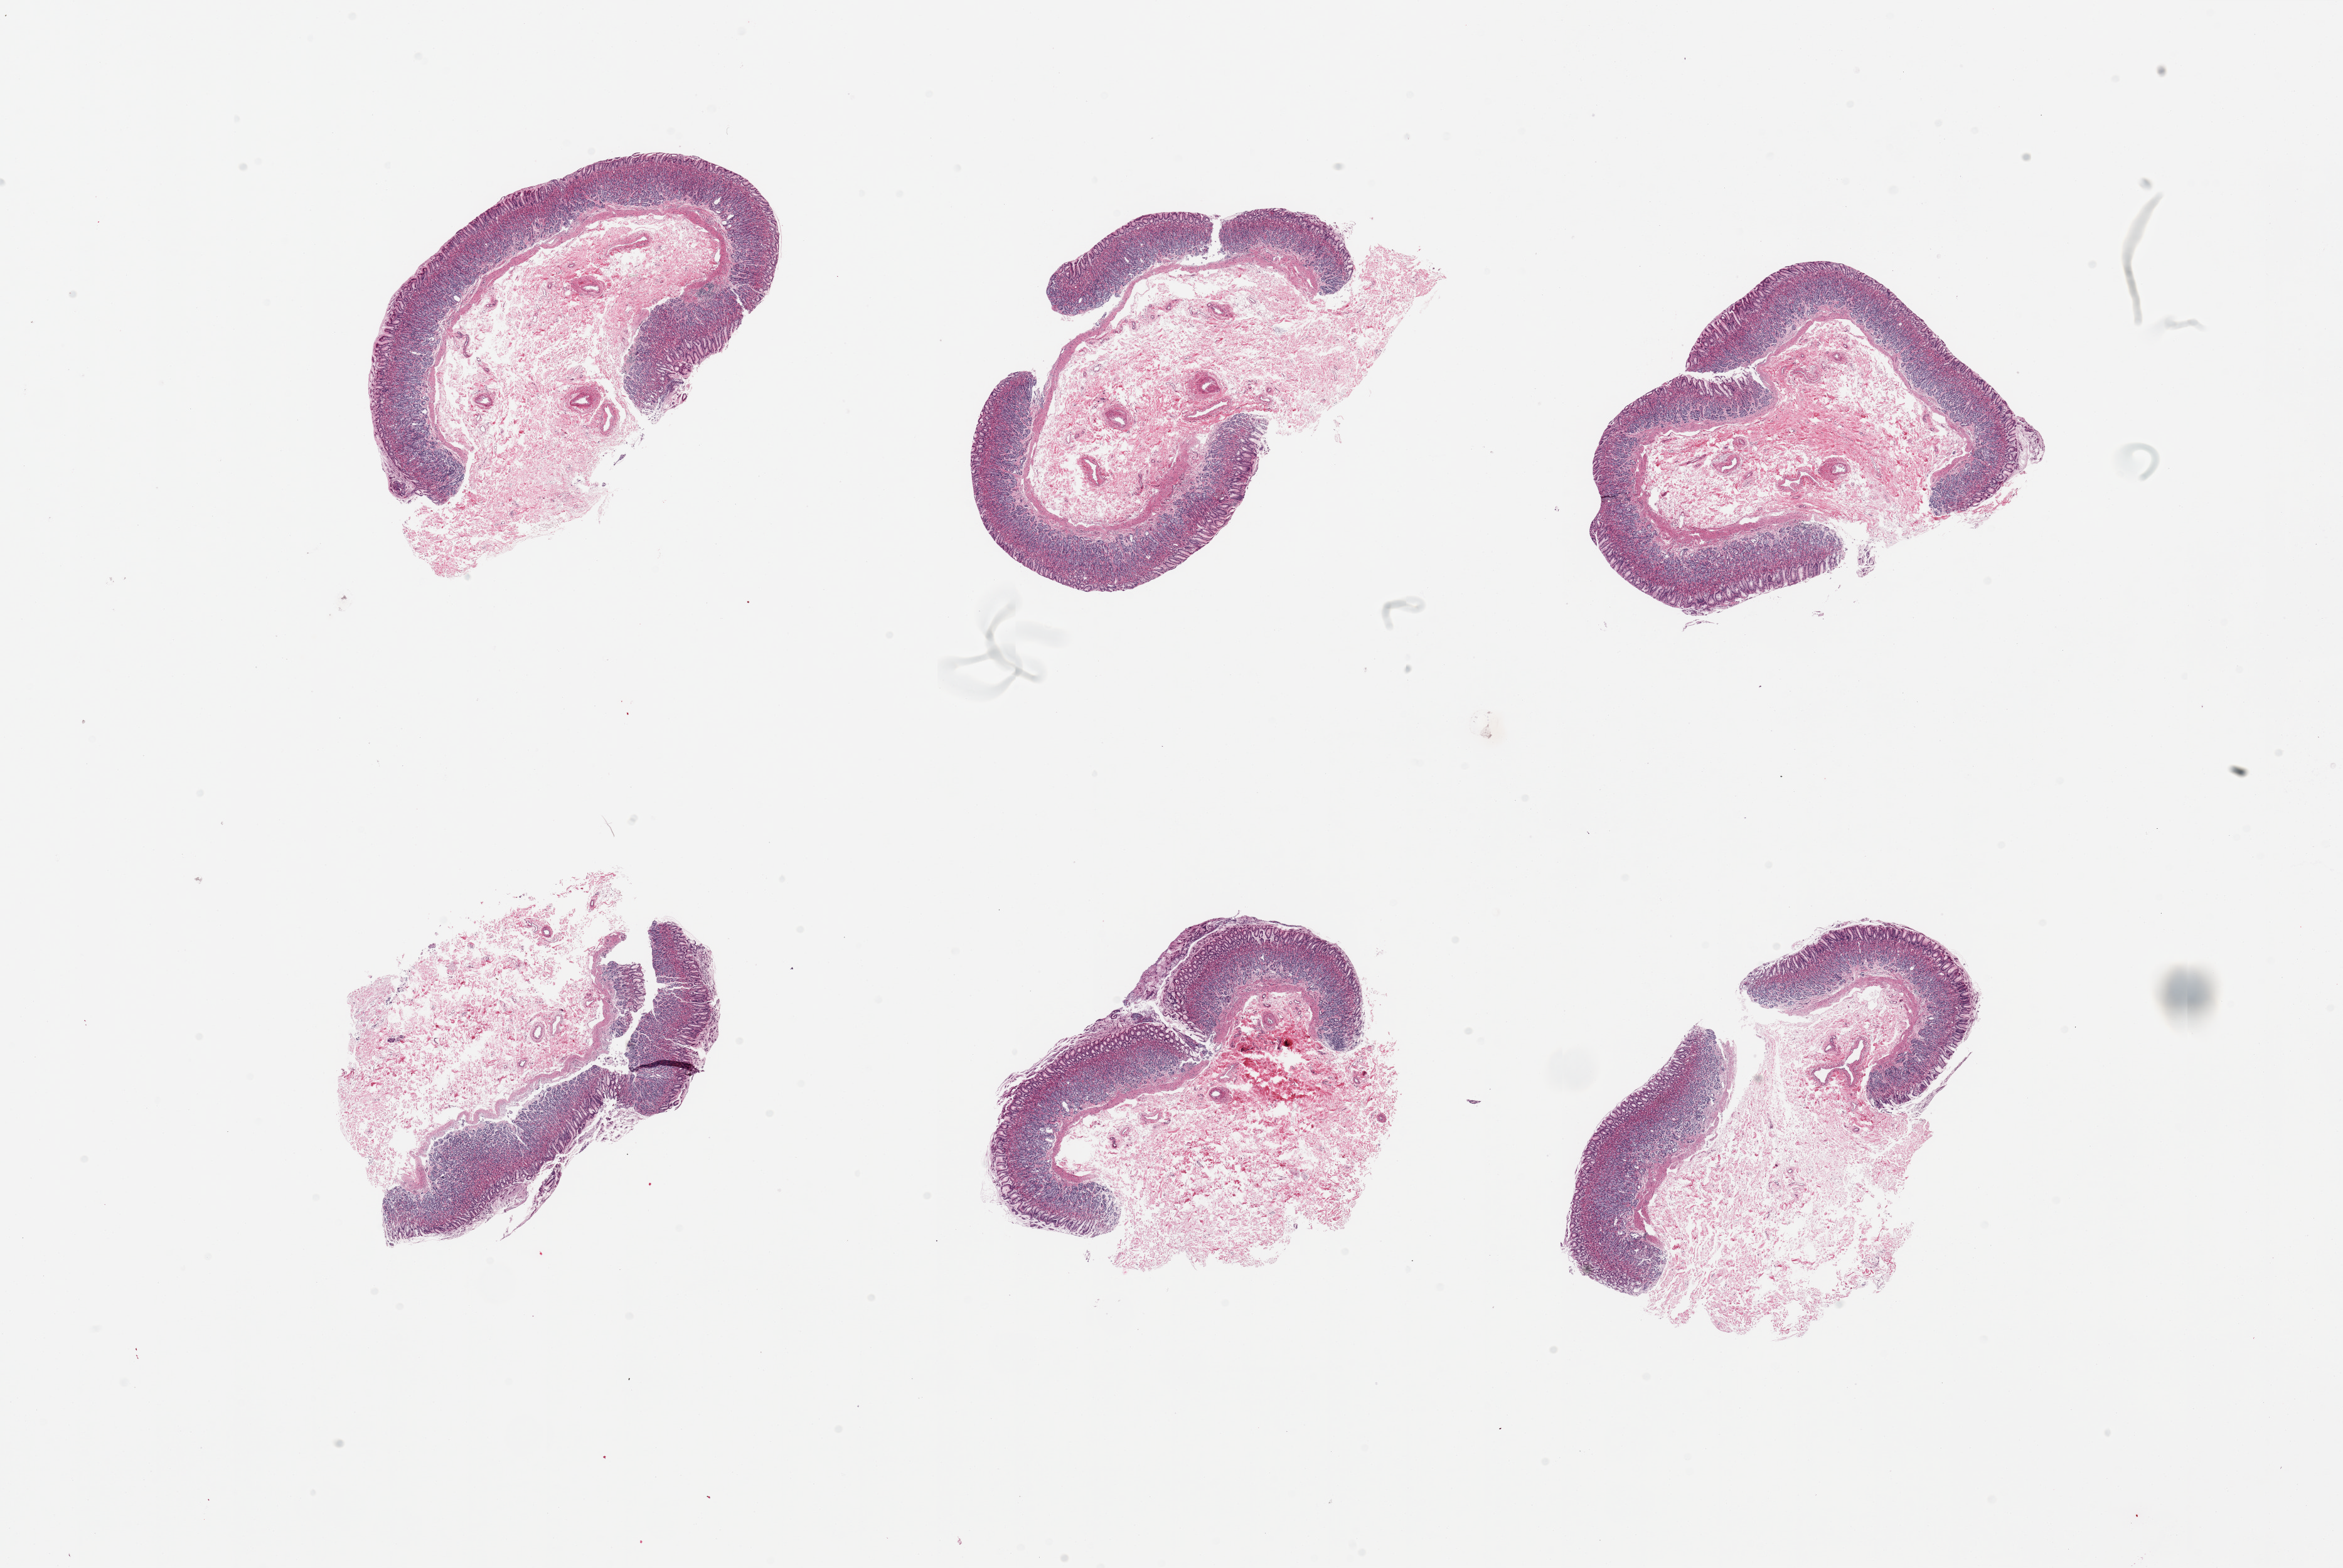
Hematoxylin and eosin (H&E) whole-slide image, shown as a low-resolution overview of the whole scanned area (about 29.5 x 19.8 mm, from a 20x scan), PAXgene-fixed paraffin-embedded (PFPE) section, target tissue: stomach, donor tissue sample. Male donor.
Review note (as recorded): 6 pieces; well preserved mucosa and submucosa, no muscularis.